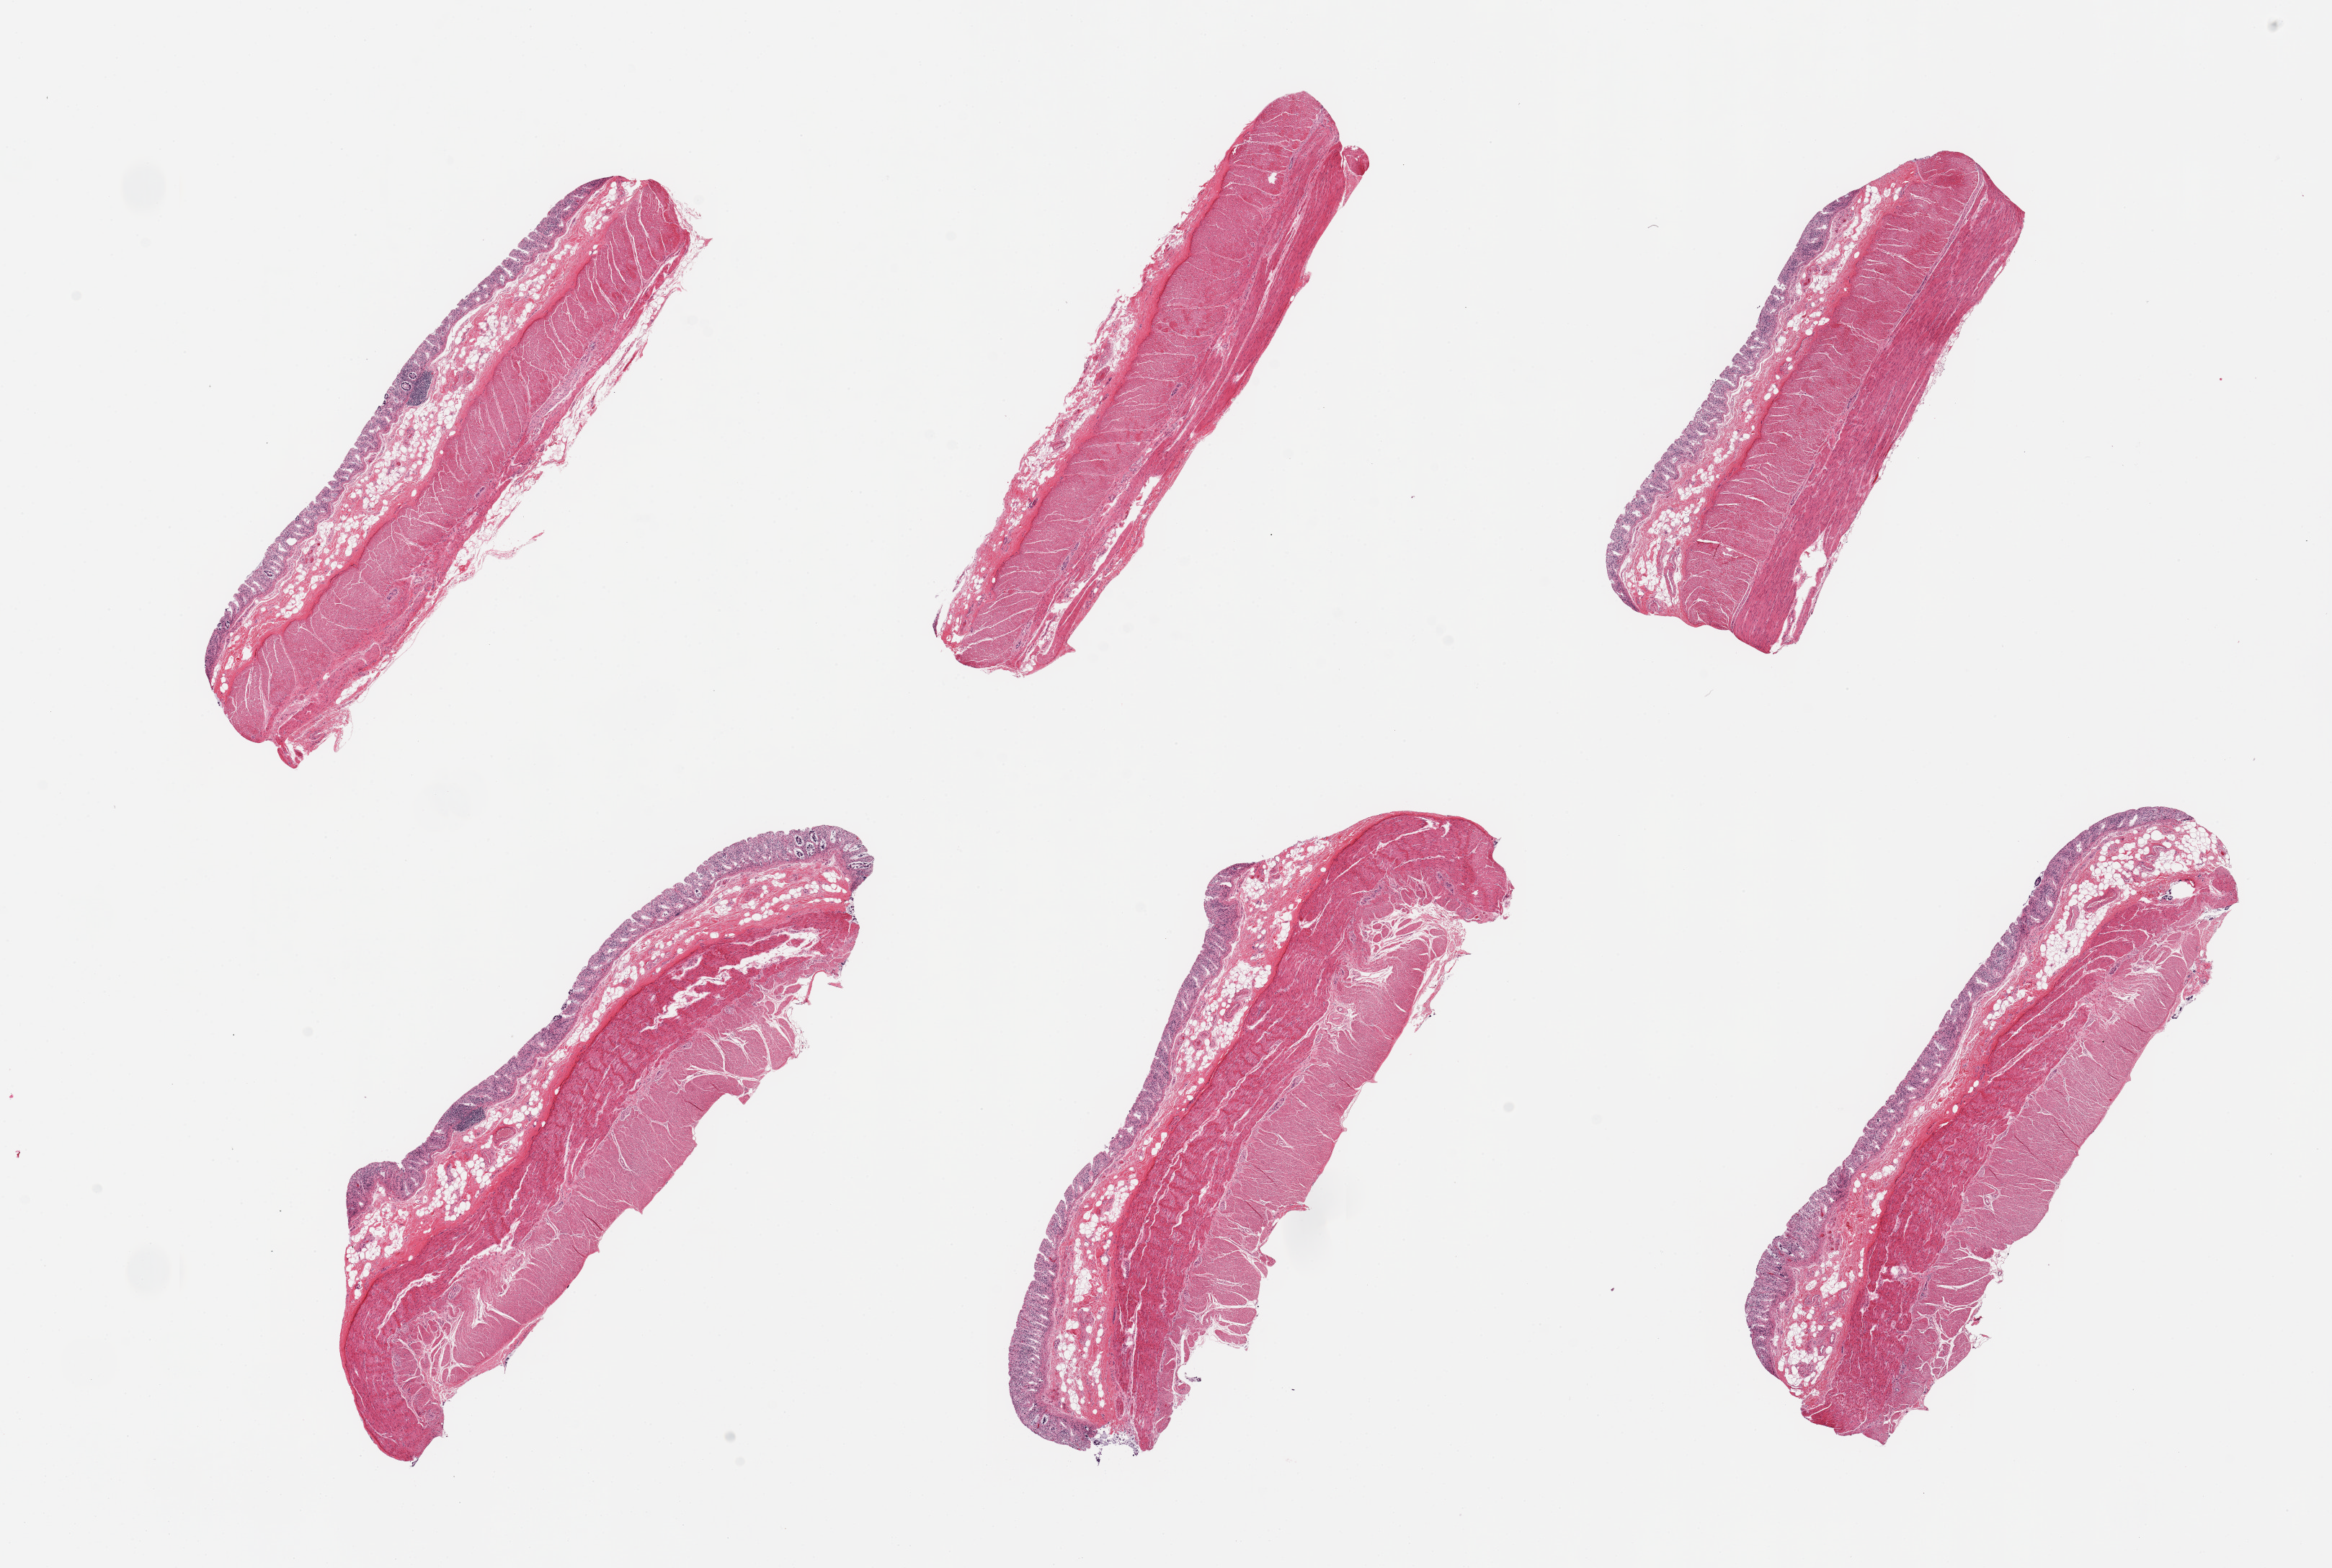
Whole-slide image, haematoxylin and eosin stain — a low-resolution overview of the entire scanned area, about 25.6 x 17.2 mm. PAXgene-fixed paraffin-embedded (PFPE) section. Section of transverse colon (target tissue). Donor tissue sample. Male donor.
* pathologist's review note for this sample: 6 pieces; 5 are full thickness, one lacks mucosa, mucosa is severely autolyzed